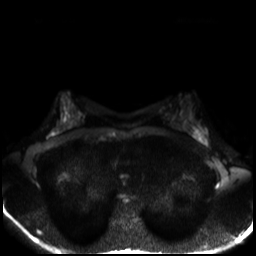
Breast MRI, one axial slice; slice 17 of 30 in the series (ordered by position); diffusion-weighted series; image 2 of 4 stored at this slice position (different b-values; order by instance number); 3 T; 4 mm slice thickness; 256 × 256 image matrix, field of view 320 × 320 mm. Female patient.
Structures marked on this image (manually delineated by an expert):
- tumour on diffusion-weighted imaging: box from (x=195, y=131) to (x=202, y=139) px